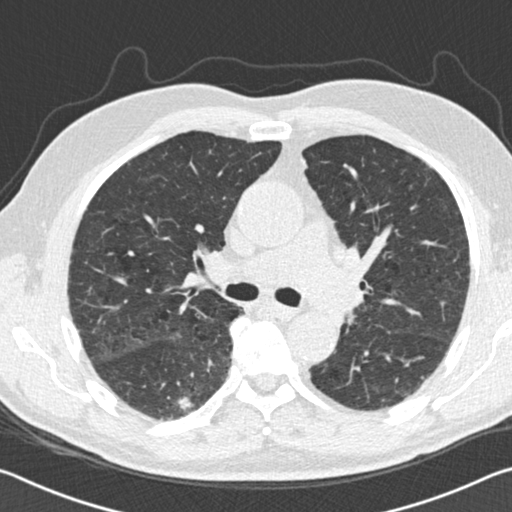
Low-dose screening chest CT, one axial slice; slice 84 of 142 in the series (ordered by position); lung window (W 1500 / L -600 HU); 2 mm slice thickness; 512 × 512 image matrix.
Structures marked on this image (manually delineated by an expert):
- lesion 1 (tumor, lower lobe of right lung): bounding box <177,396,192,412> (left, top, right, bottom; pixels)